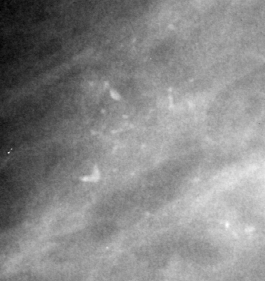
Cropped region of a digitized screen-film mammogram centred on a radiologist-marked abnormality, right breast, MLO view, BI-RADS breast density category 2 (scale 1–4).
Marked abnormality: calcifications, morphology pleomorphic, distribution clustered; BI-RADS assessment category 4; pathology (as recorded): malignant.